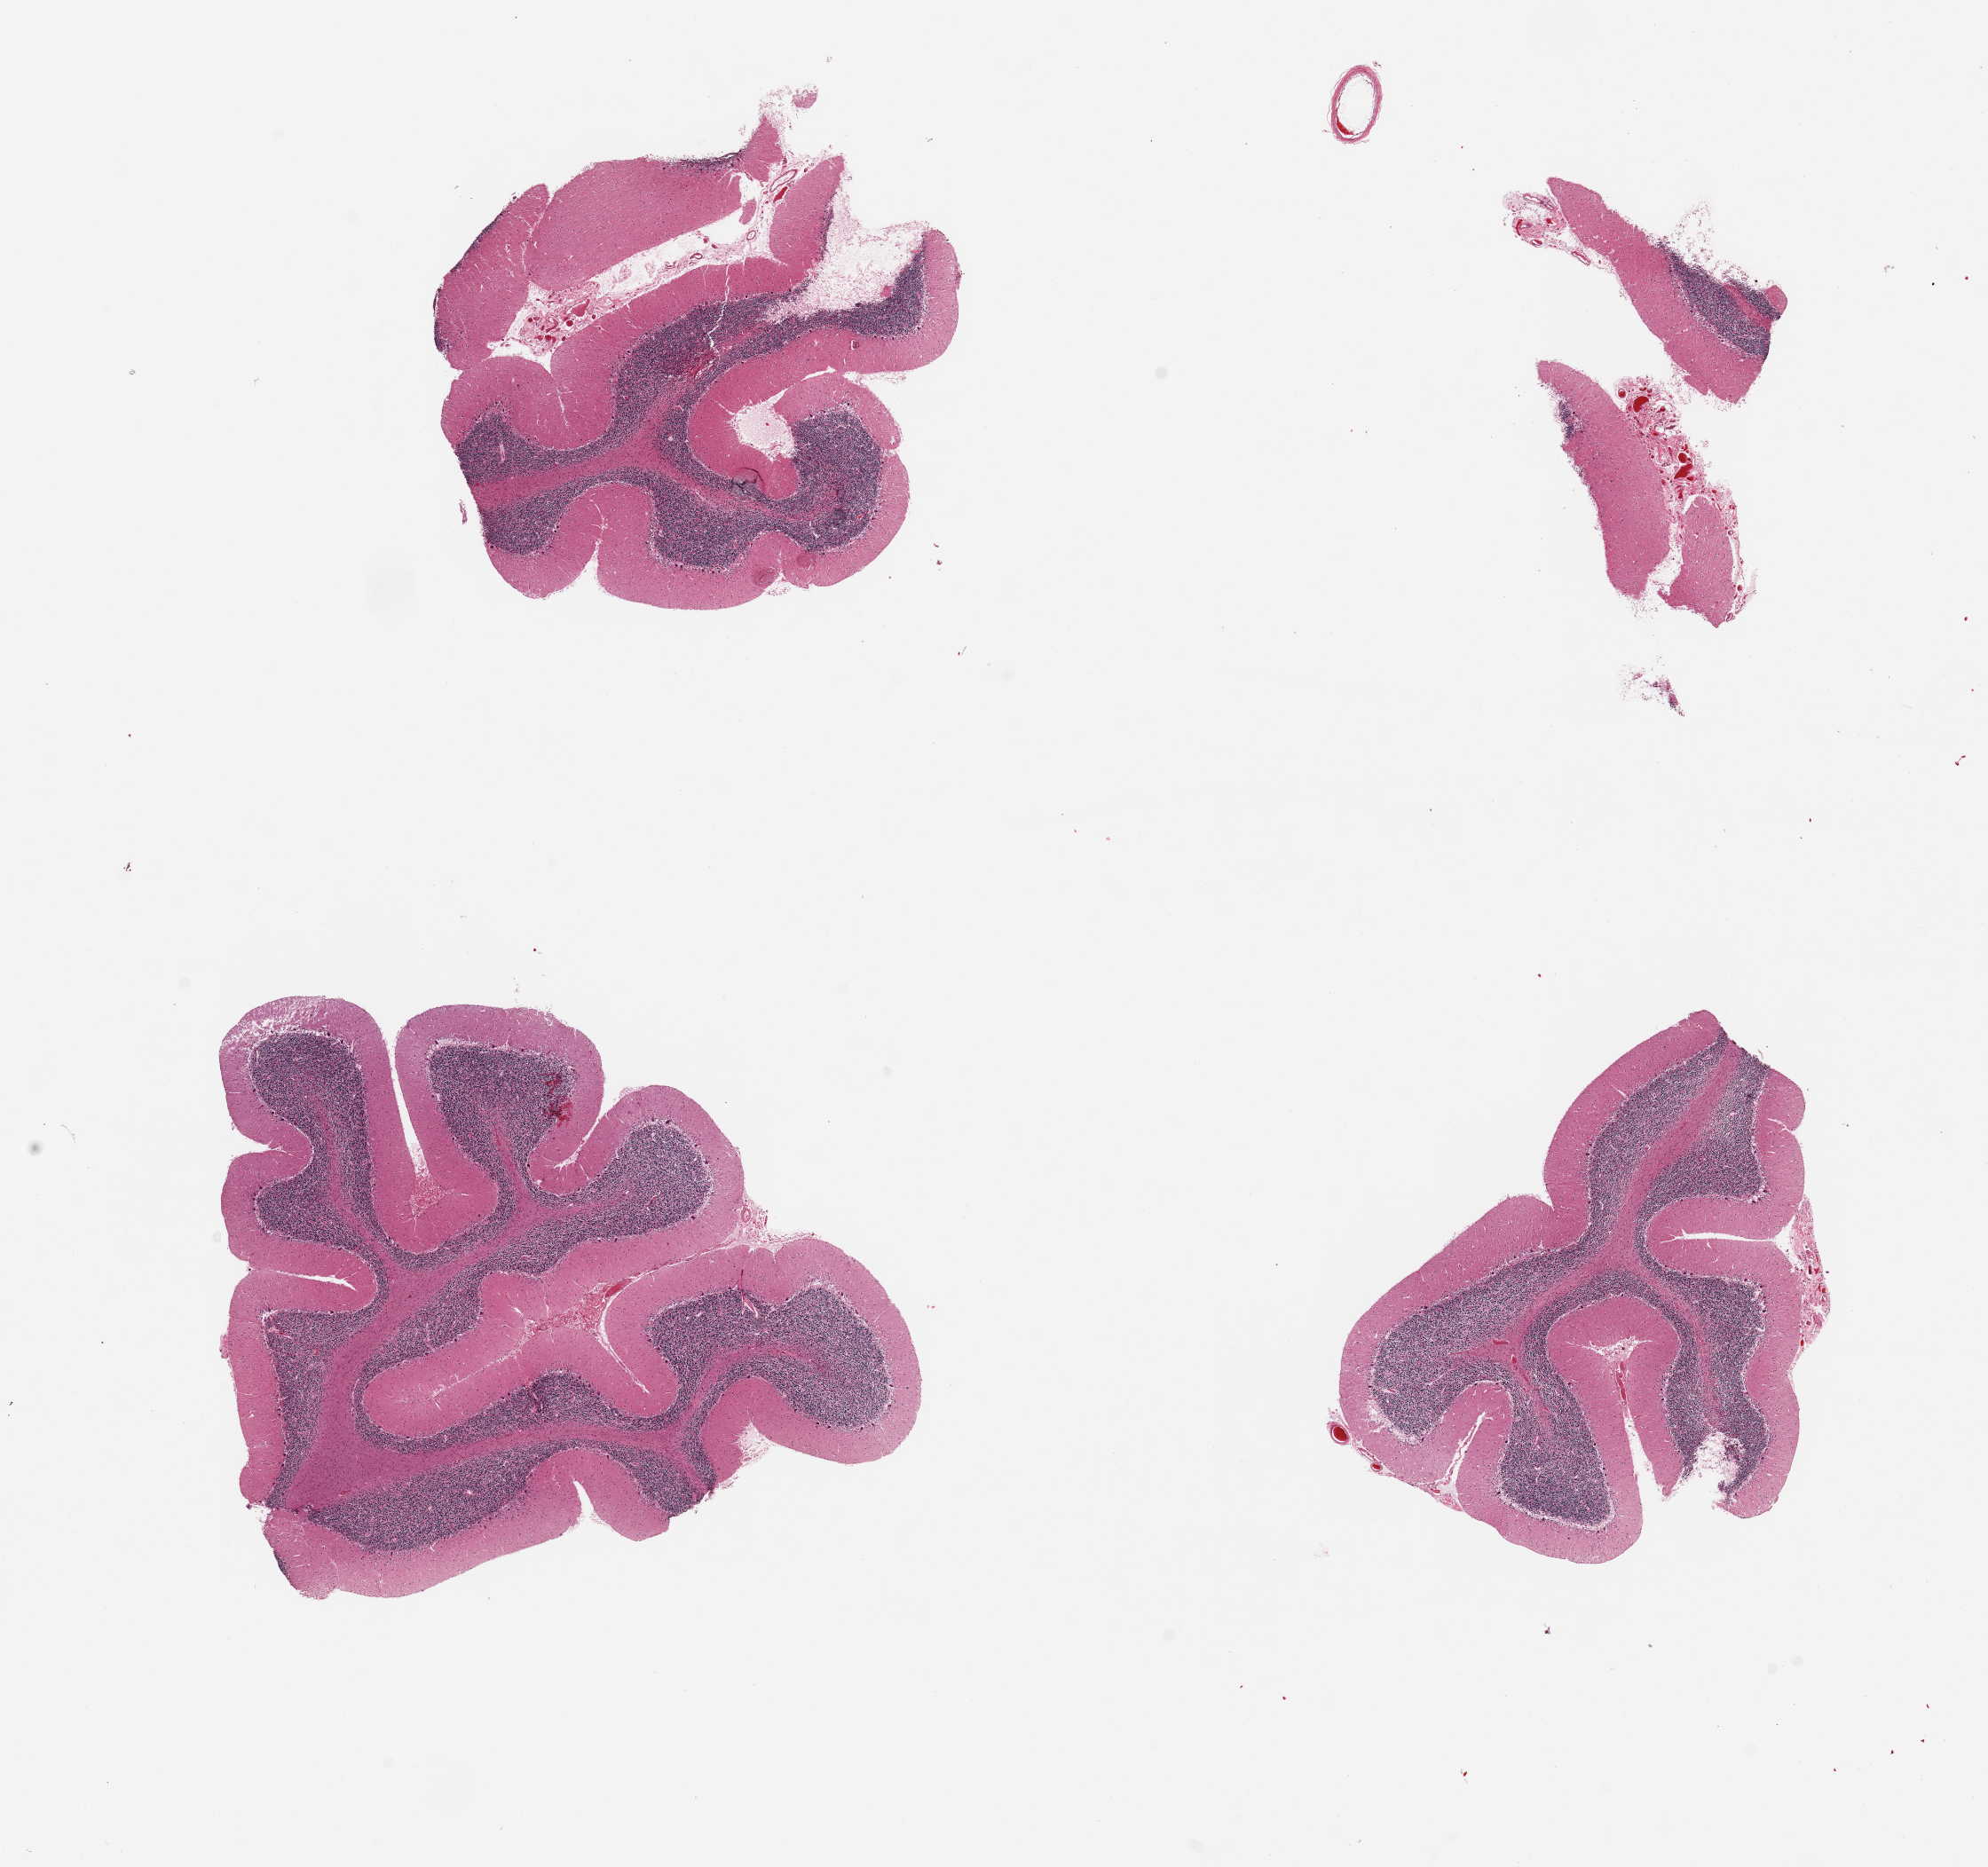
H&E whole-slide image, brightfield — low-resolution overview of the scanned area, about 17.7 x 16.6 mm; PAXgene-fixed paraffin-embedded (PFPE) section; target tissue: cerebellum; donor tissue sample. Donor: male.
Reviewer comment on this tissue sample: 4 pieces, moderately autolyzed; Purkinje cells do not show significant hypoxic damage.